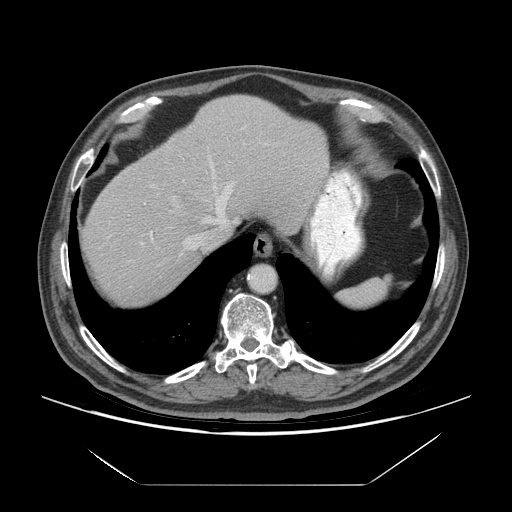
Contrast-enhanced abdominal CT (liver protocol), one axial slice. Position 58 of 75 along the scan axis. Reconstruction kernel STANDARD. Soft-tissue window (W 400 / L 40 HU). 2.5 mm slice thickness. 512 × 512 image matrix, field of view 420 × 420 mm. Case-level facts recorded for this patient, not image findings: diagnosis: hepatocellular carcinoma (patient treated with transarterial chemoembolisation; whether this scan precedes or follows treatment is not stated here); TNM stage (as recorded): Stage-I; Child-Pugh class: A; tumour differentiation: well differentiated; tumour nodularity: uninodular.
Outlined on this slice (semi-automatic segmentation, software-assisted and operator-edited):
- abdominal aorta: bounding box (x1, y1, x2, y2) in pixels: (250, 266, 275, 291)
- liver parenchyma outside the tumour (the mass and vessels are separate outlines, so this box may not span the whole liver): (82, 96, 328, 304)
- mass: (182, 194, 208, 216)
- liver vessels: (141, 127, 245, 255)